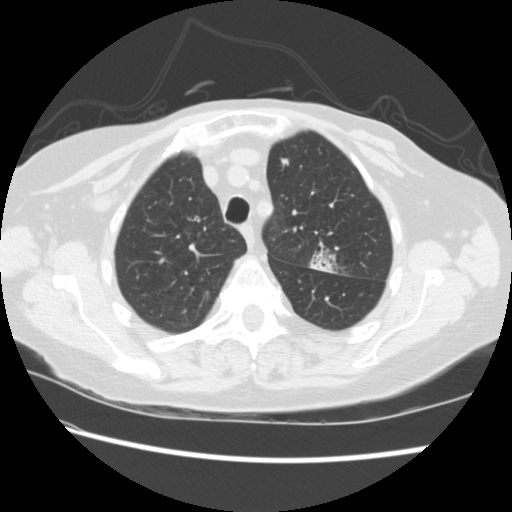
Low-dose screening chest CT, one axial slice. Position 170 of 224 along the scan axis. Lung window (W 1500 / L -600 HU). 512 × 512 image matrix, field of view 340 × 340 mm.
Structures marked on this image (manually delineated by an expert):
- lesion 1 (tumor, upper lobe of left lung): bounding box (x1, y1, x2, y2) in pixels: (310, 249, 336, 273)